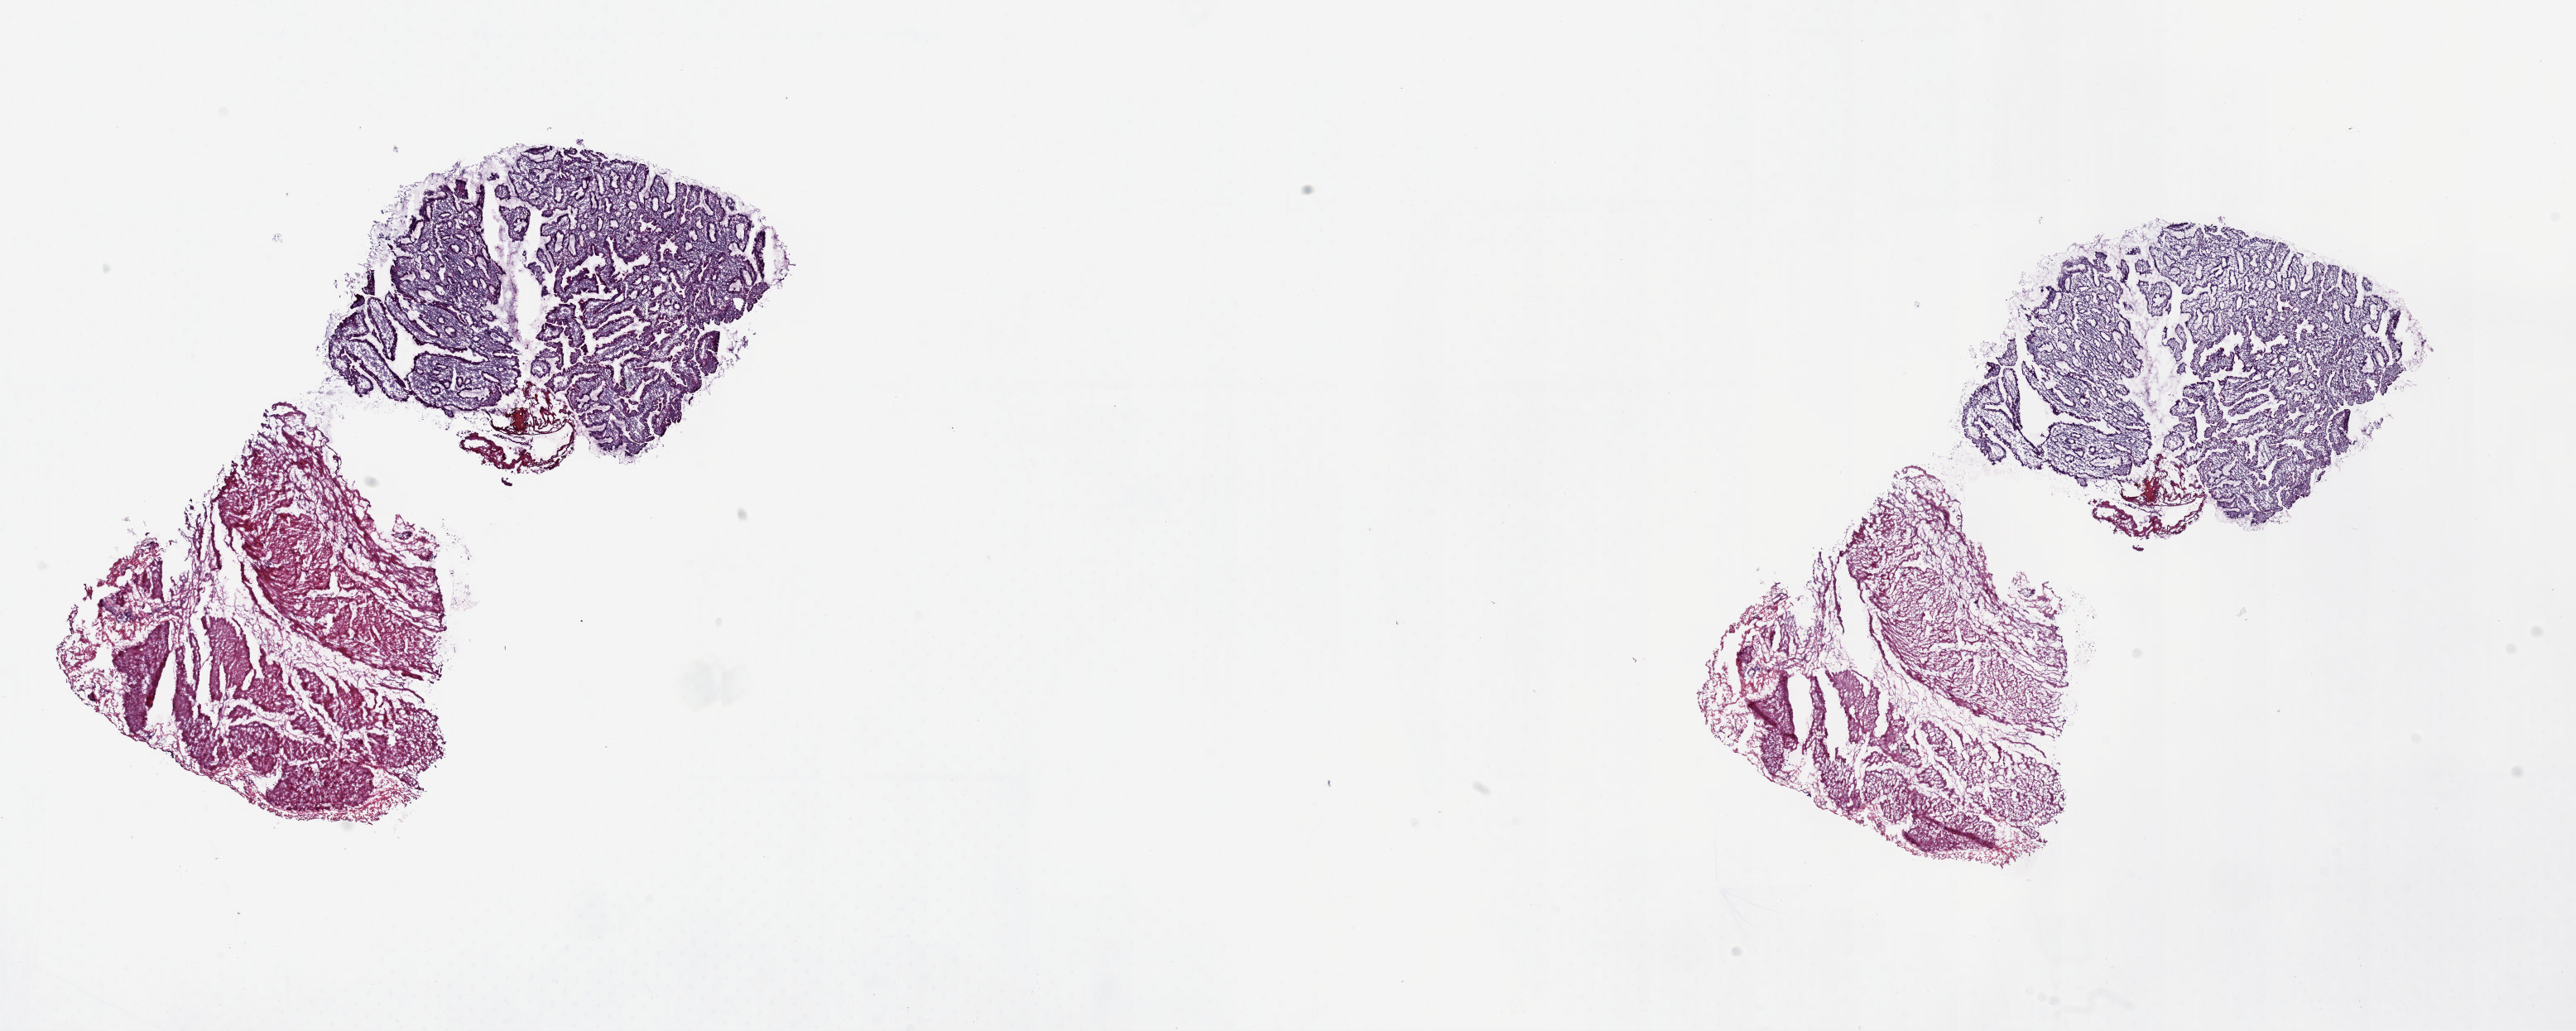
Whole-slide histology image, H&E — low-resolution overview of the scanned area, about 24.5 x 9.8 mm. Frozen section from the top of the tissue portion. Sample: solid tissue normal (non-tumour tissue), stomach. Male patient; age at initial diagnosis 61 years. Slide review estimates, as recorded: tumour cells 0%, tumour nuclei 0%, normal cells 100%, stromal cells 0%, necrosis 0%. Infiltration values recorded for this section: lymphocyte infiltration 15%, monocyte infiltration 1%, neutrophil infiltration 2%.
This section: solid tissue normal sample (biorepository sample class). Patient diagnosis: Tubular adenocarcinoma (gastric antrum).